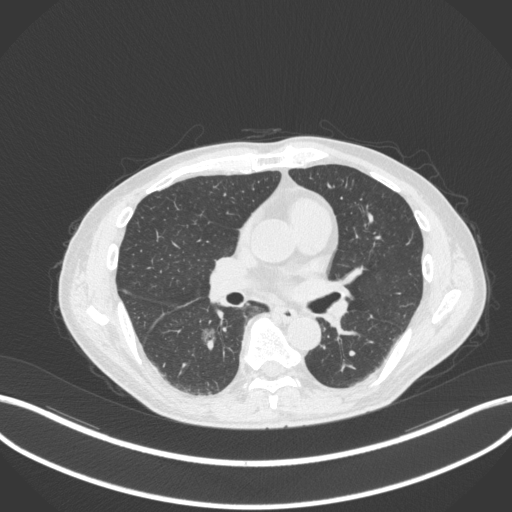
Chest CT, one axial slice; slice 169 of 324 in the series (ordered by position); lung window (W 1500 / L -600 HU); 512 × 512 image matrix, field of view 400 × 400 mm. Male patient, age 61 years. Case-level facts recorded for this patient, not image findings: clinical TNM (as recorded): T1c N0 M0.
Annotated regions visible in this slice (rectangle marked by the reading radiologist):
- lung tumour (recorded histology: adenocarcinoma): bounding box [x1, y1, x2, y2] px = [195, 323, 222, 353]